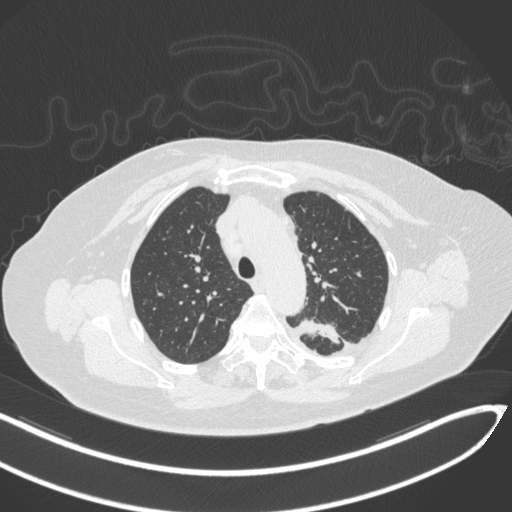
Chest CT, one axial slice; slice 235 of 270 in the series (ordered by position); lung window (W 1500 / L -600 HU); 1 mm slice thickness; 512 × 512 image matrix. Patient: female, 76 years. From the clinical record (not read from this slice): clinical TNM (as recorded): T1c N0 M0.
Annotated regions visible in this slice (bounding box drawn by a radiologist):
- lung tumour (recorded histology: adenocarcinoma): bounding box (x1, y1, x2, y2) in pixels: (290, 314, 347, 351)